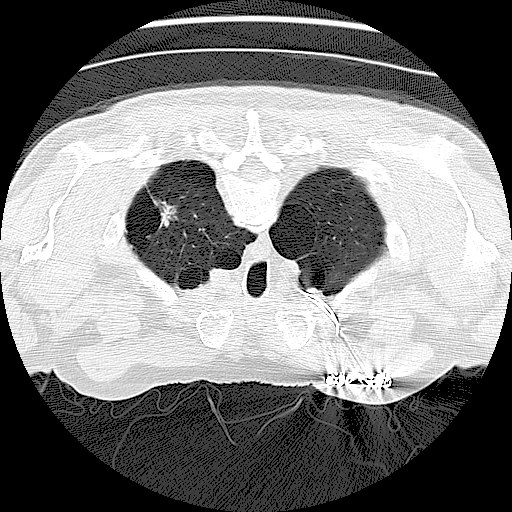
Low-dose screening chest CT, one axial slice; lung window (W 1500 / L -600 HU); 512 × 512 image matrix, field of view 330 × 330 mm.
Outlined on this slice (manually delineated by an expert):
- lesion 1 (tumor): box from (x=155, y=200) to (x=178, y=229) px